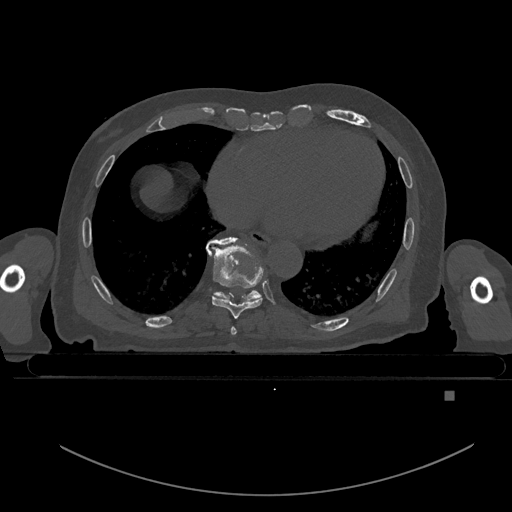
CT including the spine, one axial slice. Position 188 of 969 along the scan axis. Bone window (W 1800 / L 400 HU). 0.5 mm slice thickness. 512 × 512 image matrix, field of view 456 × 456 mm. Male patient, age 82 years. From the clinical record (not read from this slice): primary cancer: prostate.
Outlined on this slice (semi-automatic segmentation, software-assisted and operator-edited):
- T7 vertebra: bounding box (x1, y1, x2, y2) in pixels: (231, 326, 236, 335)
- T8 vertebra: (209, 239, 263, 319)
- T9 vertebra: (206, 236, 262, 301)